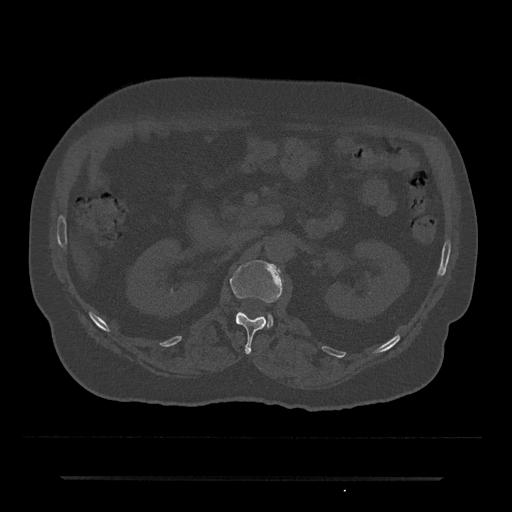
CT including the spine, one axial slice; slice 57 of 797 in the series (ordered by position); reconstruction kernel Br40s/3; bone window (W 1800 / L 400 HU); 0.5 mm slice thickness; 512 × 512 image matrix, field of view 437 × 437 mm. Male patient, age 69 years. Case-level facts recorded for this patient, not image findings: primary cancer: prostate.
Outlined on this slice (semi-automatic segmentation, software-assisted and operator-edited):
- L1 vertebra: bounding box <230,260,284,354> (left, top, right, bottom; pixels)
- L2 vertebra: <267,314,273,328>